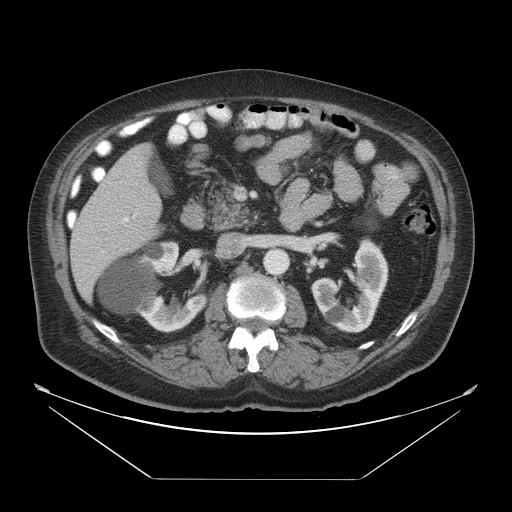
Contrast-enhanced abdominal CT, one axial slice. Slice 21 of 45 in the series (ordered by position). Reconstruction kernel STANDARD. 120 kVp. Intravenous contrast given. Soft-tissue window (W 400 / L 40 HU). 5 mm slice thickness. 512 × 512 image matrix. Male patient, age 87 years. Case-level facts recorded for this patient, not image findings: diagnosis: colorectal cancer liver metastases, imaged before liver resection; multiple liver metastases: no; largest metastasis: 4.5 cm; disease in both lobes: yes.
Outlined on this slice (outlined manually by an expert reader):
- liver: bounding box [x1, y1, x2, y2] px = [70, 144, 165, 302]
- portal vein (with intrahepatic branches): [122, 181, 137, 221]